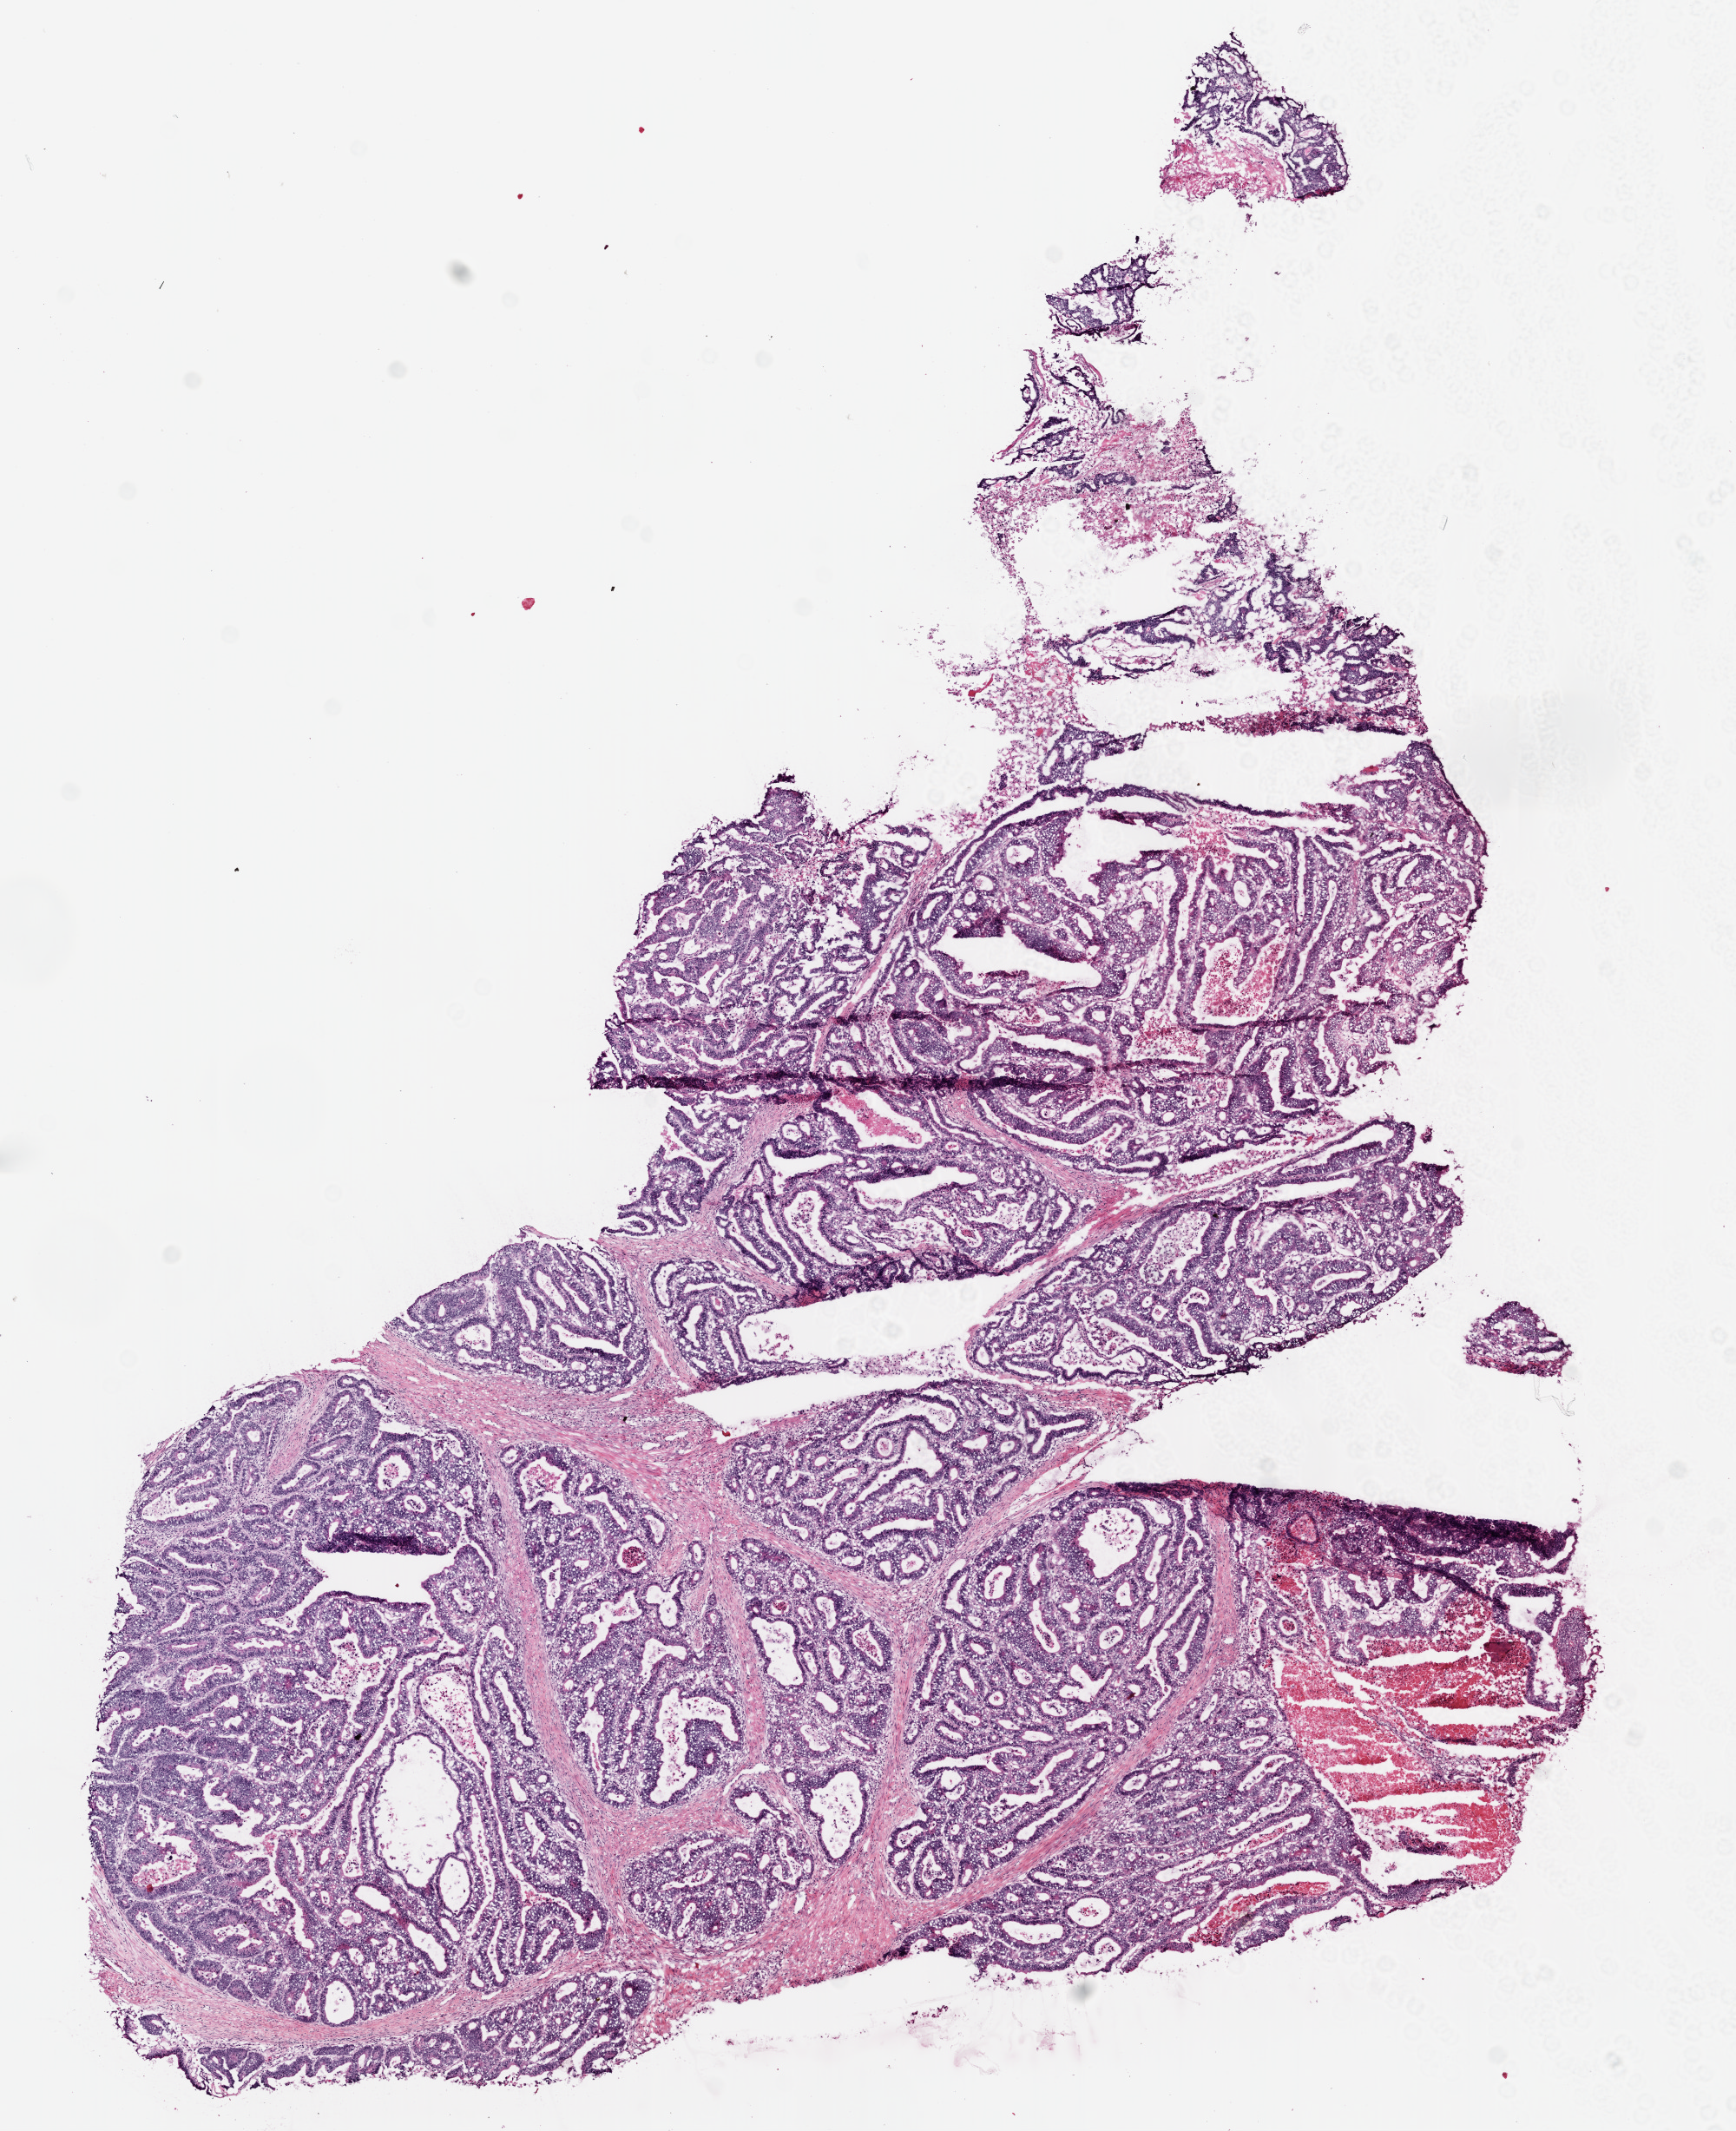
Whole-slide histology image, Hematoxylin and eosin (H&E) stained, whole scanned area (about 8.0 x 9.8 mm) shown as a low-resolution overview; frozen section from the top of the tissue portion; primary tumour sample from the rectum. Patient: male, age at initial diagnosis 54 years. Composition of this section per pathologist review: tumour cells 75%, tumour nuclei 80%, normal cells 0%, stromal cells 15%, necrosis 10%.
AJCC pathologic stage: IIB (7th edition). Diagnosis: Adenocarcinoma, NOS. TNM: T4a N0 M0.